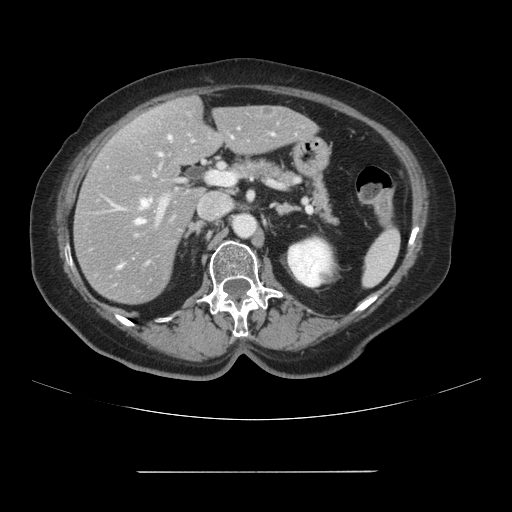
Contrast-enhanced abdominal CT, one axial slice. Intravenous contrast given. Soft-tissue window (W 400 / L 40 HU). 2.5 mm slice thickness. 512 × 512 image matrix, field of view 400 × 400 mm. Female patient, age 74 years. From the clinical record (not read from this slice): diagnosis: colorectal cancer liver metastases, imaged before liver resection; multiple liver metastases: yes; largest metastasis: 1.1 cm; disease in both lobes: yes.
Outlined on this slice (expert manual segmentation):
- hepatic veins: bounding box [x1, y1, x2, y2] px = [136, 137, 171, 224]
- liver: [75, 98, 316, 304]
- planned liver remnant (the part of the liver to remain after resection): [143, 97, 316, 165]
- portal vein (with intrahepatic branches): [134, 122, 304, 236]
- liver metastasis: [262, 106, 272, 115]